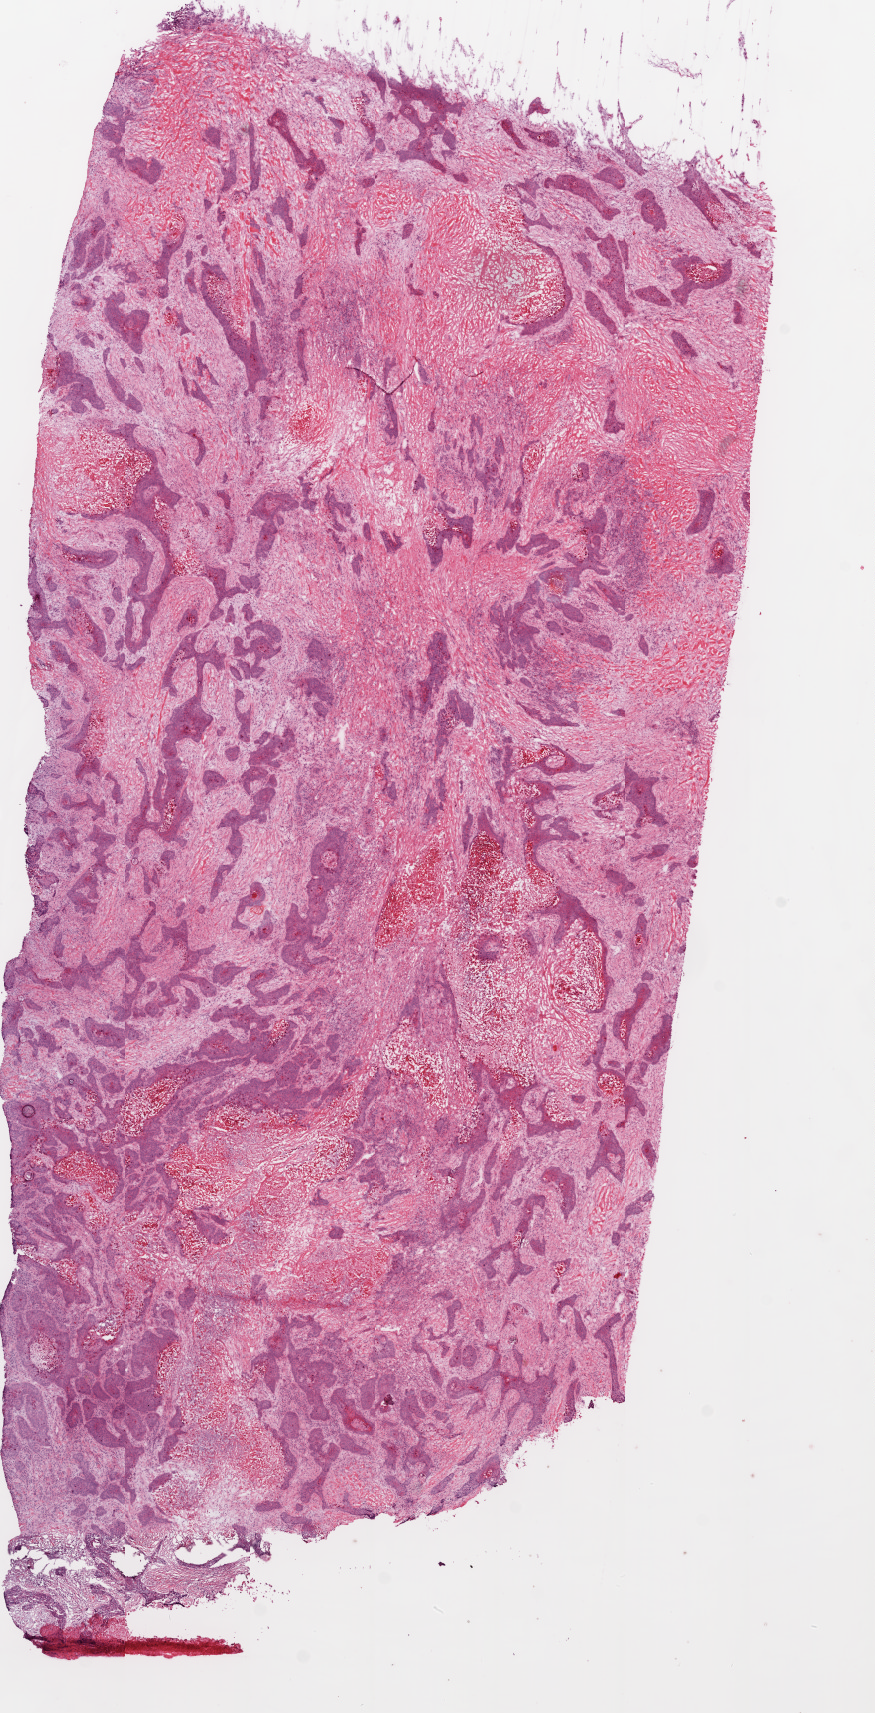
Digitized H&E-stained tissue section (whole slide) — whole scanned area (about 7.0 x 13.7 mm) shown as a low-resolution overview; frozen section; sample: primary tumour, lung. Patient: male, age at initial diagnosis 73 years. Slide review estimates, as recorded: tumour cells 38%, tumour nuclei 60%, normal cells 2%, stromal cells 40%, necrosis 20%.
- diagnosis: Squamous cell carcinoma, NOS (upper lobe, lung)
- AJCC pathologic stage: IIA